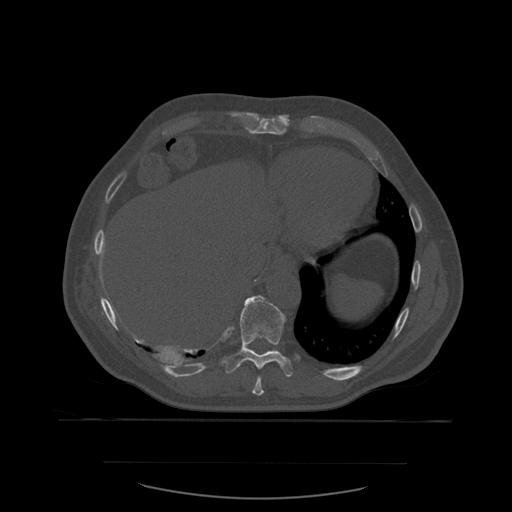
CT including the spine, one axial slice. Position 320 of 590 along the scan axis. Bone window (W 1800 / L 400 HU). 512 × 512 image matrix, field of view 479 × 479 mm. Patient age 71 years. Case-level facts recorded for this patient, not image findings: primary cancer: lung.
Structures marked on this image (semi-automatic segmentation, software-assisted and operator-edited):
- T10 vertebra: bounding box [x1, y1, x2, y2] px = [226, 296, 293, 377]
- T9 vertebra: [252, 377, 265, 396]